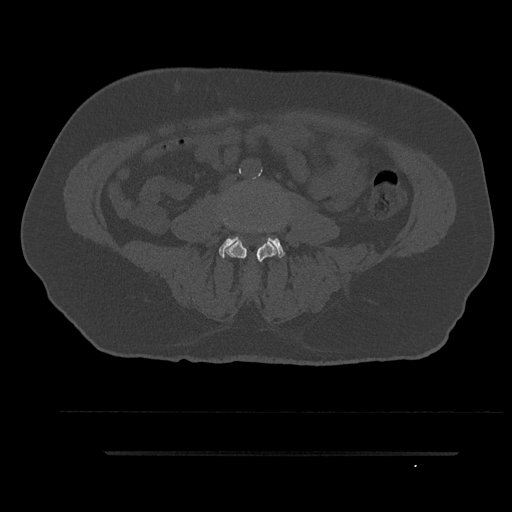
CT including the spine, one axial slice. Reconstruction kernel Br40s/3. Bone window (W 1800 / L 400 HU). 0.5 mm slice thickness. 512 × 512 image matrix. Male patient, age 63 years. Case-level facts recorded for this patient, not image findings: primary cancer: renal; vertebrae with lytic lesions (as recorded): T8.
Structures marked on this image (semi-automatically segmented with operator editing):
- L3 vertebra: bounding box [x1, y1, x2, y2] px = [220, 198, 286, 285]
- L4 vertebra: [219, 236, 285, 258]